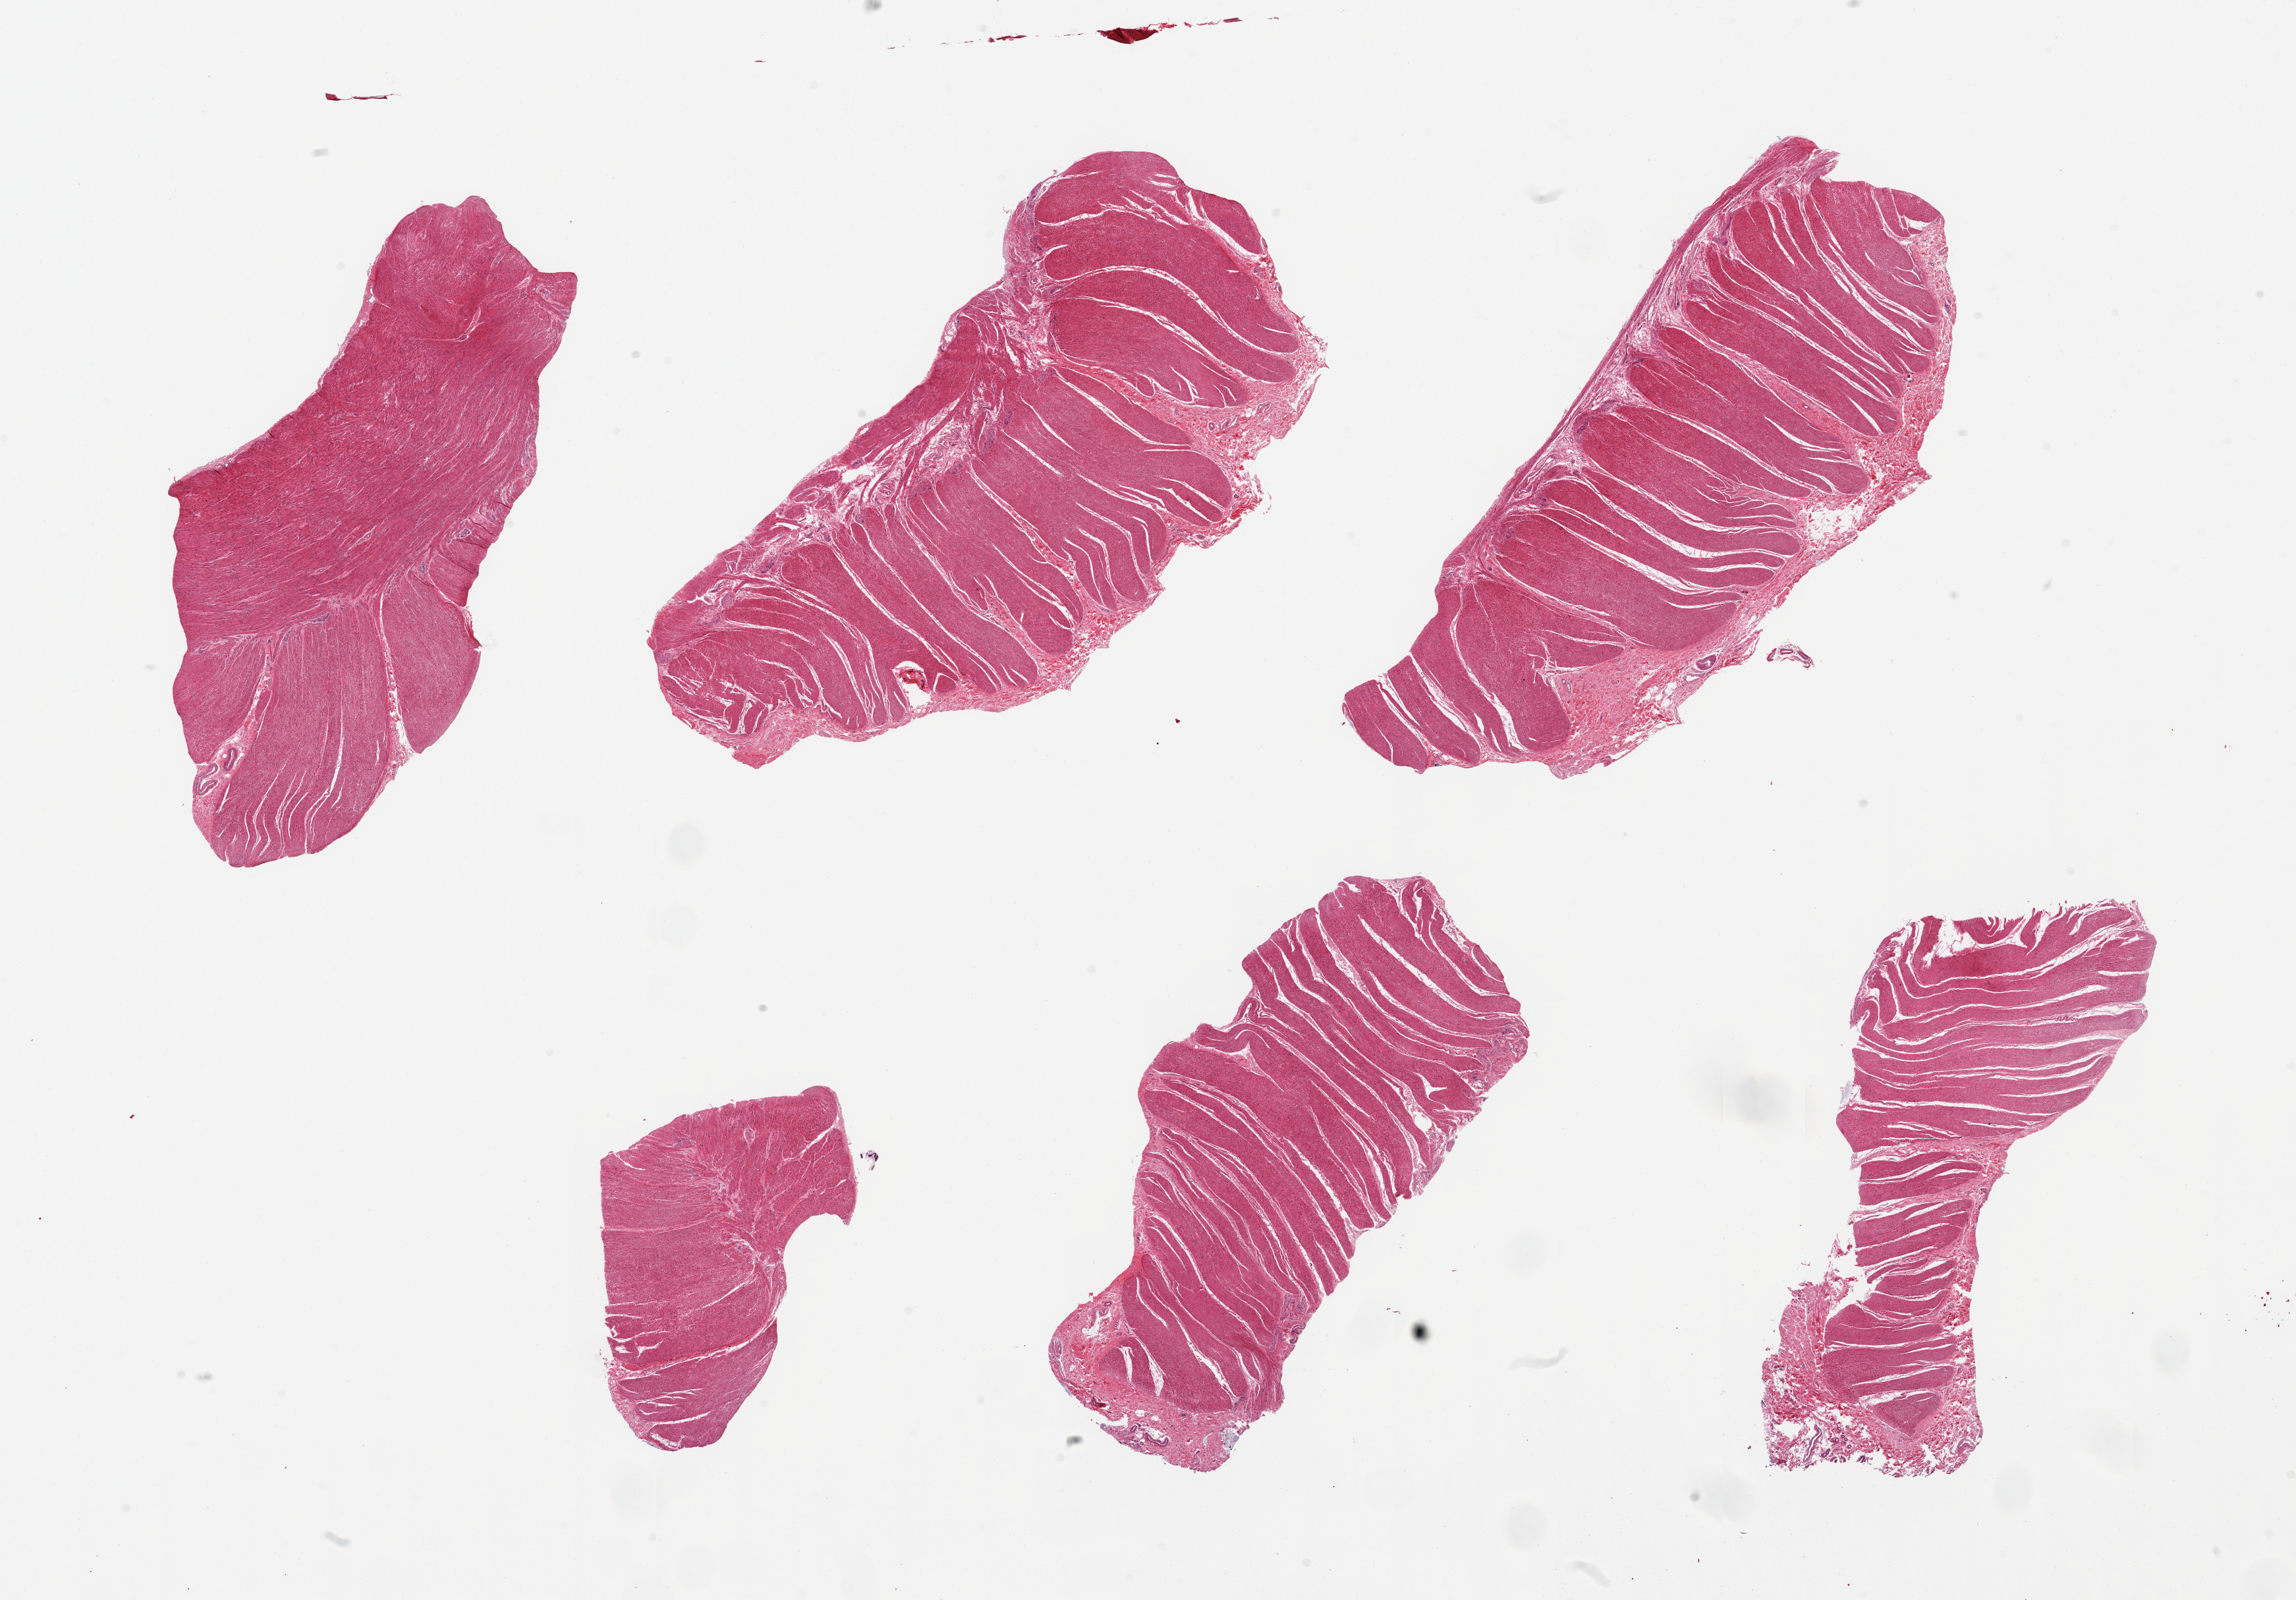
Digitized H&E-stained section, low-resolution overview of the scanned area, about 27.6 x 19.2 mm, PAXgene-fixed paraffin-embedded (PFPE) section, section of sigmoid colon (target tissue), tissue donor sample. Male donor.
Review note (as recorded): 6 pieces; target muscularis.